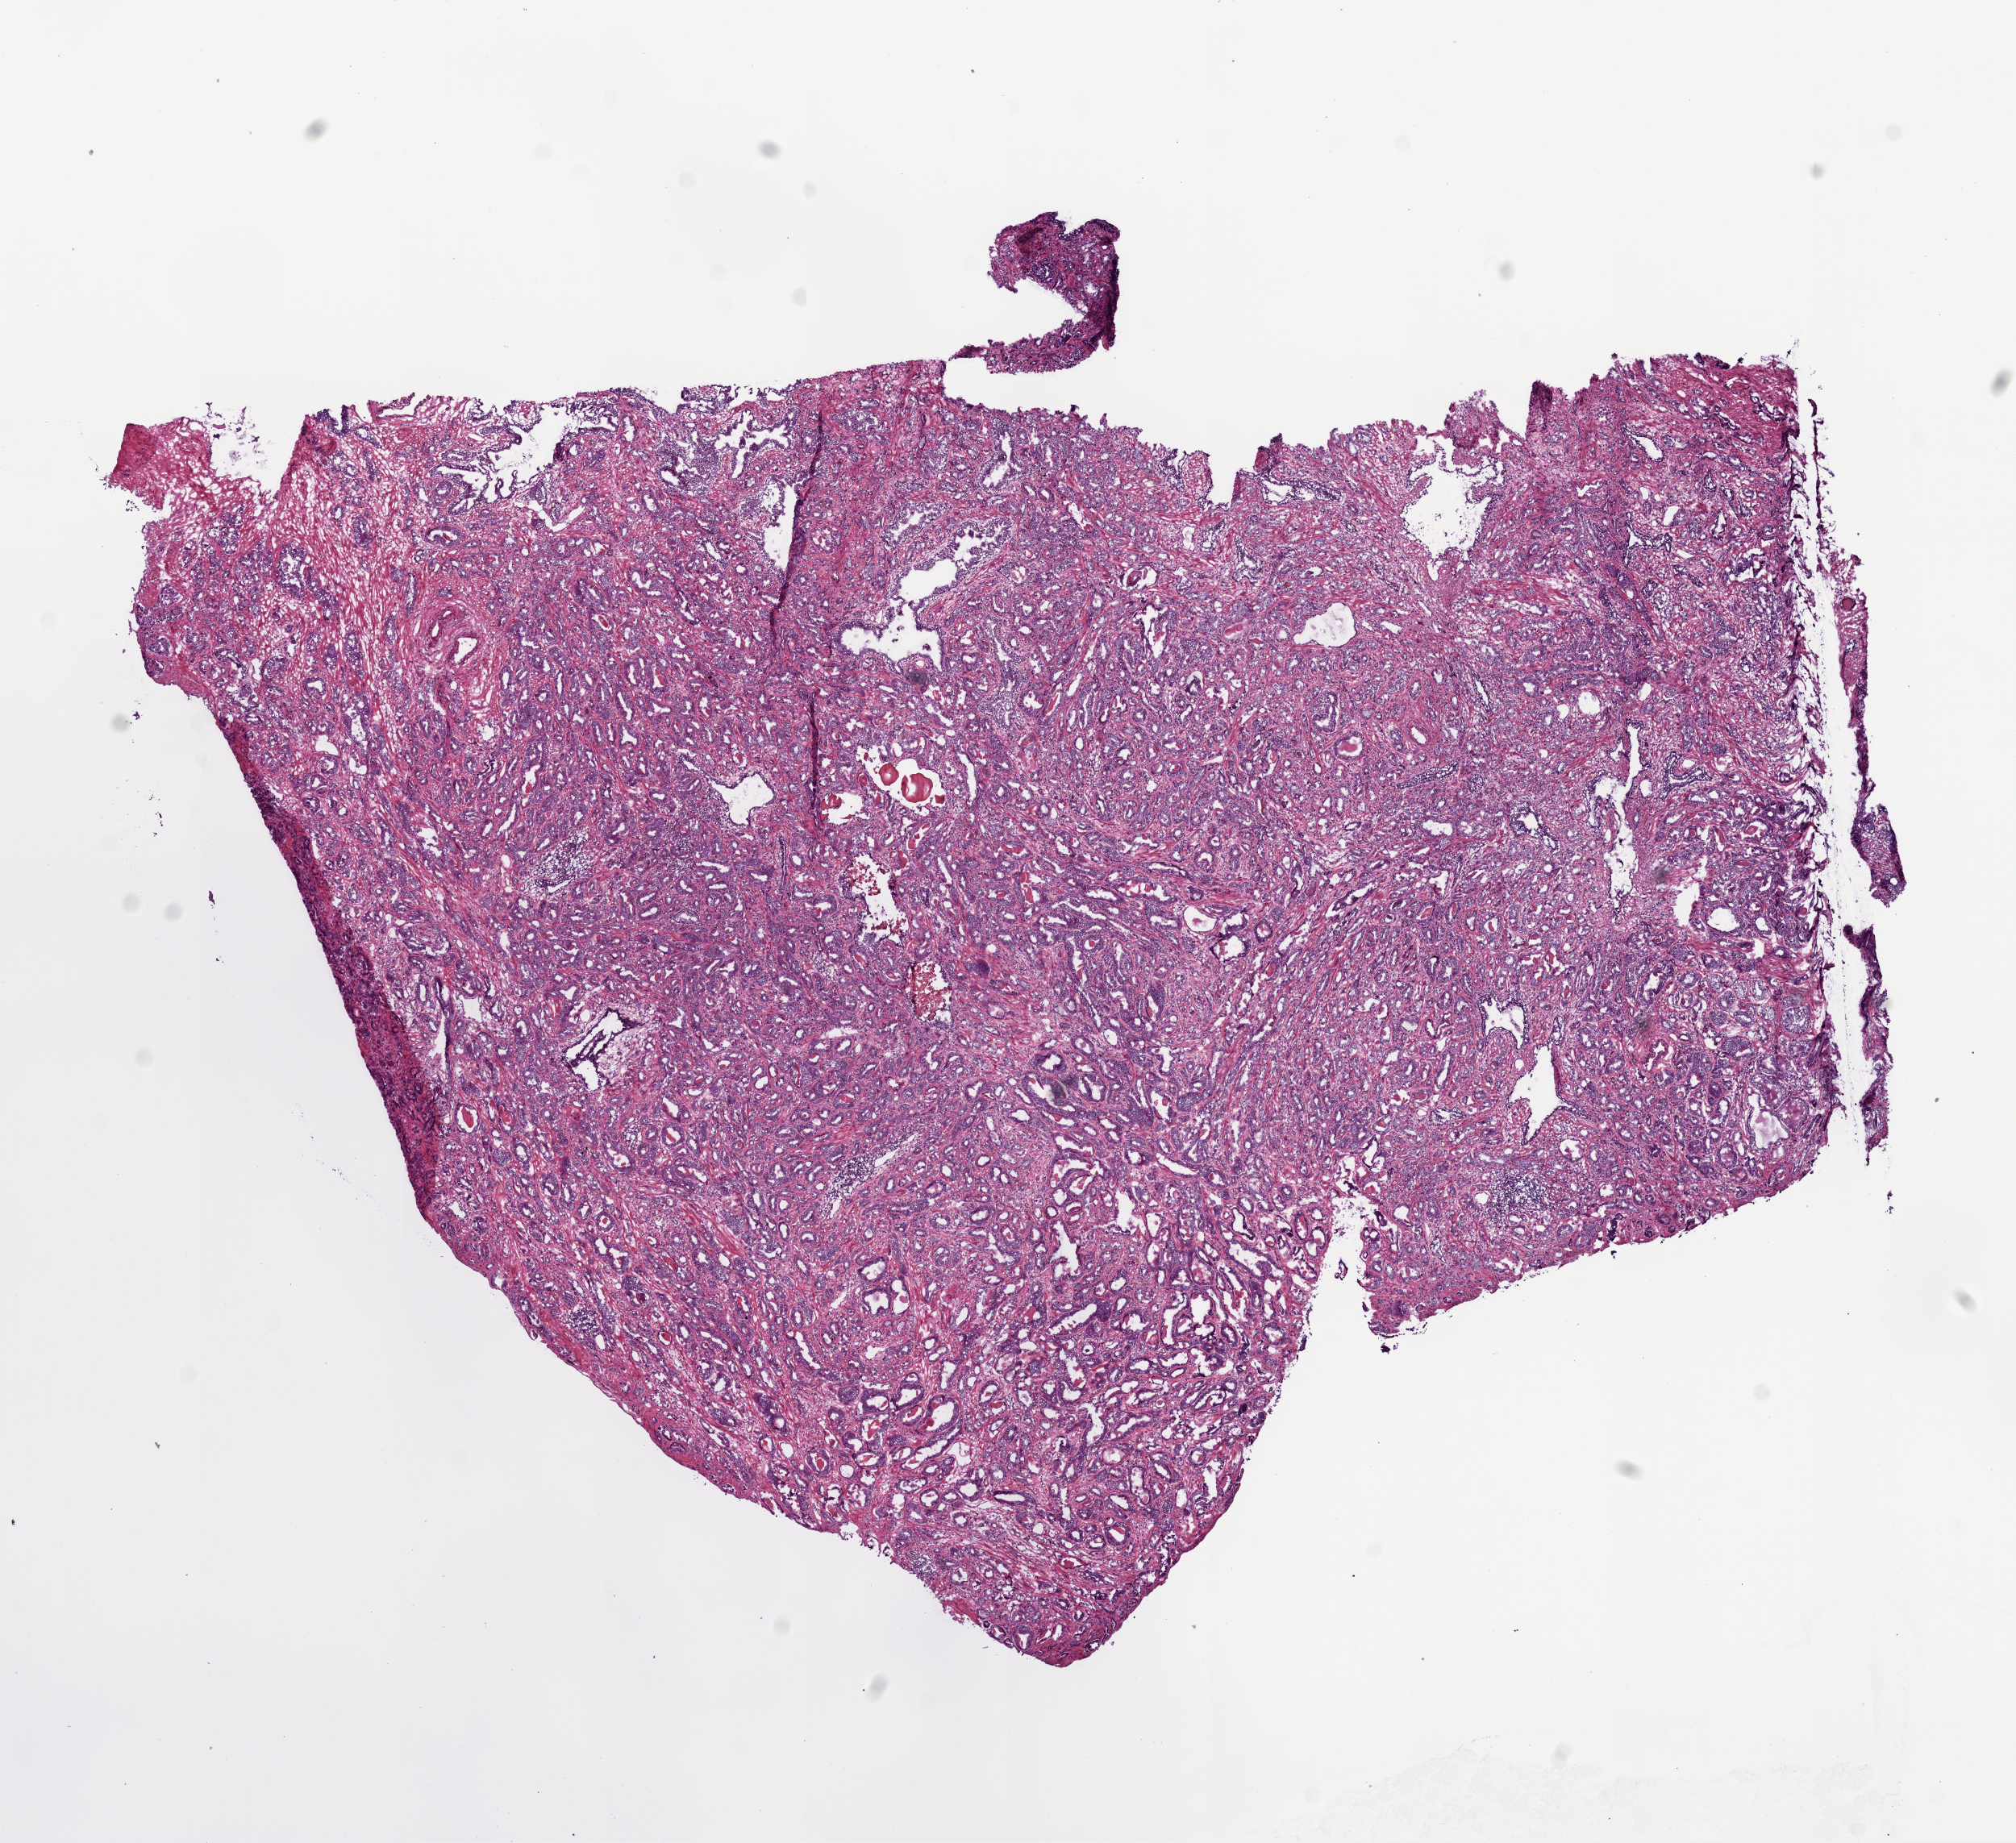
Hematoxylin and eosin (H&E) stained whole-slide image — whole scanned area (about 10.0 x 9.2 mm, slide scanned at 20x) shown as a low-resolution overview. Frozen section from the bottom of the tissue portion. Sample: primary tumour, prostate. Patient: male, age at initial diagnosis 63 years. Gleason score: 7 (3+4). Composition of this section per pathologist review: tumour cells 70%, tumour nuclei 75%, normal cells 10%, stromal cells 19%, necrosis 1%. Infiltration values recorded for this section: lymphocyte infiltration 2%, monocyte infiltration 1%, neutrophil infiltration 2%.
Pathologic diagnosis: Acinar cell carcinoma (prostate gland). Laterality: bilateral. Lymph nodes positive (case pathology): 0 of 10 examined.